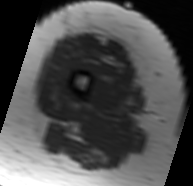
MRI of an extremity soft-tissue mass, one axial slice. Slice 14 of 91 in the series (ordered by position). MR volume resampled by the dataset authors to the PET/CT grid (not the native acquisition matrix). 3.27 mm slice thickness. 193 × 186 image matrix. Female patient. Case-level facts recorded for this patient, not image findings: histological type: malignant solitary fibrous tumor; grade: intermediate; site of the primary tumour: right thigh.
Structures marked on this image (expert contour drawn on MRI and transferred to this co-registered scan by the dataset authors):
- gross tumour volume including surrounding oedema: bounding box [x1, y1, x2, y2] px = [72, 37, 125, 72]